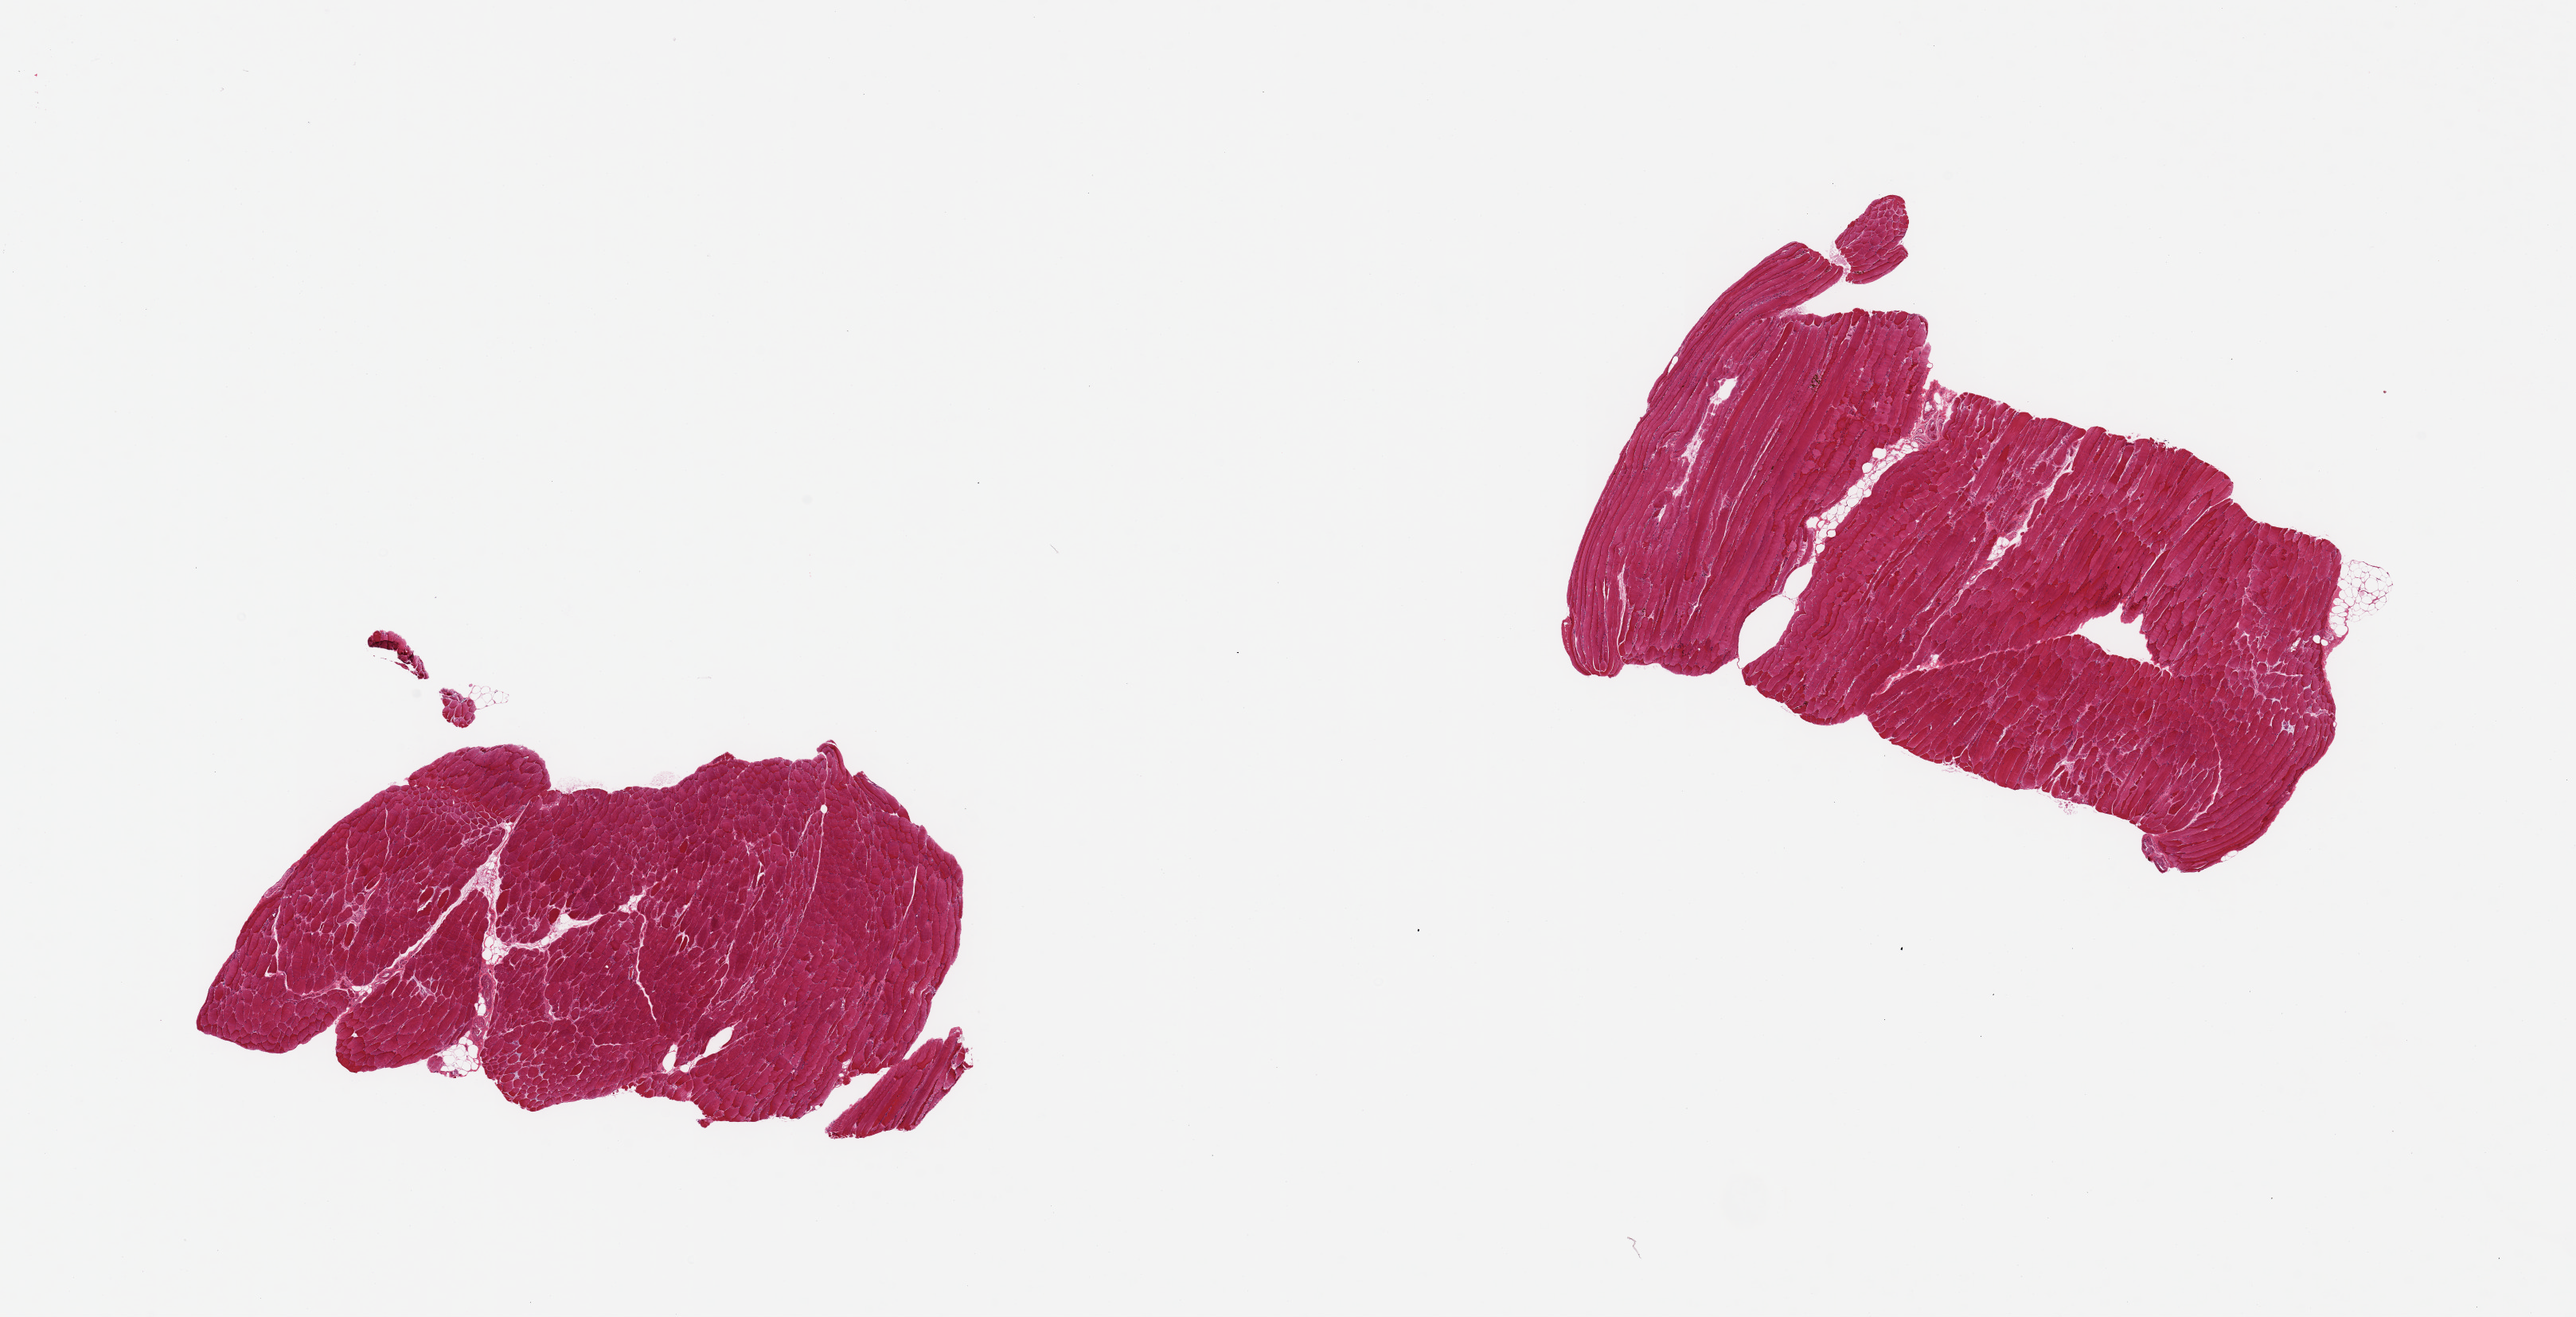
Digitized hematoxylin and eosin (H&E)-stained section, a low-resolution overview of the entire scanned area, about 25.6 x 13.1 mm; PAXgene-fixed paraffin-embedded (PFPE) section; section of skeletal muscle (target tissue); donor tissue sample.
- pathologist's review note for this sample: 2 pieces; minimal fatty content